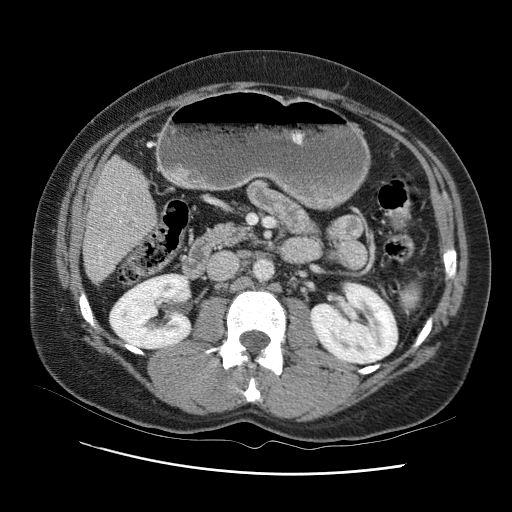
Contrast-enhanced abdominal CT (liver protocol), one axial slice. Slice 31 of 95 in the series (ordered by position). Reconstruction kernel STANDARD. 120 kVp. One of 2 acquisitions stored at this slice position. Soft-tissue window (W 400 / L 40 HU). 2.5 mm slice thickness. 512 × 512 image matrix. From the clinical record (not read from this slice): diagnosis: hepatocellular carcinoma (patient treated with transarterial chemoembolisation; whether this scan precedes or follows treatment is not stated here); TNM stage (as recorded): Stage-I; Child-Pugh class: B; tumour differentiation: moderately differentiated; tumour nodularity: uninodular.
Structures marked on this image (semi-automatic segmentation, software-assisted and operator-edited):
- liver parenchyma outside the tumour (the mass and vessels are separate outlines, so this box may not span the whole liver): bounding box [x1, y1, x2, y2] px = [84, 142, 162, 288]
- liver vessels: [99, 181, 157, 250]